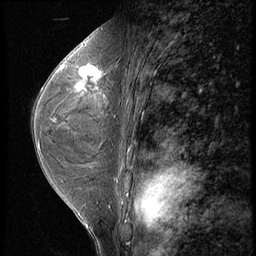
Breast MRI (dynamic contrast-enhanced), one sagittal slice. Slice 32 of 56 in the series (ordered by position). 3 images stored at this slice position (order not interpretable as contrast timing). 1.5 T. TE 4.2 ms, TR 9 ms. 2.5 mm slice thickness. 256 × 256 image matrix. Patient: female, 44 years. From the clinical record (not read from this slice): setting: breast cancer imaged before/during neoadjuvant chemotherapy; receptor status: triple-negative.
Outlined on this slice (semi-automatically segmented with operator editing):
- analysis volume of interest (the breast-tissue region the enhancement analysis was run in; not a lesion): box from (x=71, y=54) to (x=112, y=99) px
- tumour enhancement mask (voxels above the 140 % enhancement threshold inside the analysis volume of interest): (x=75, y=65)–(x=102, y=91)